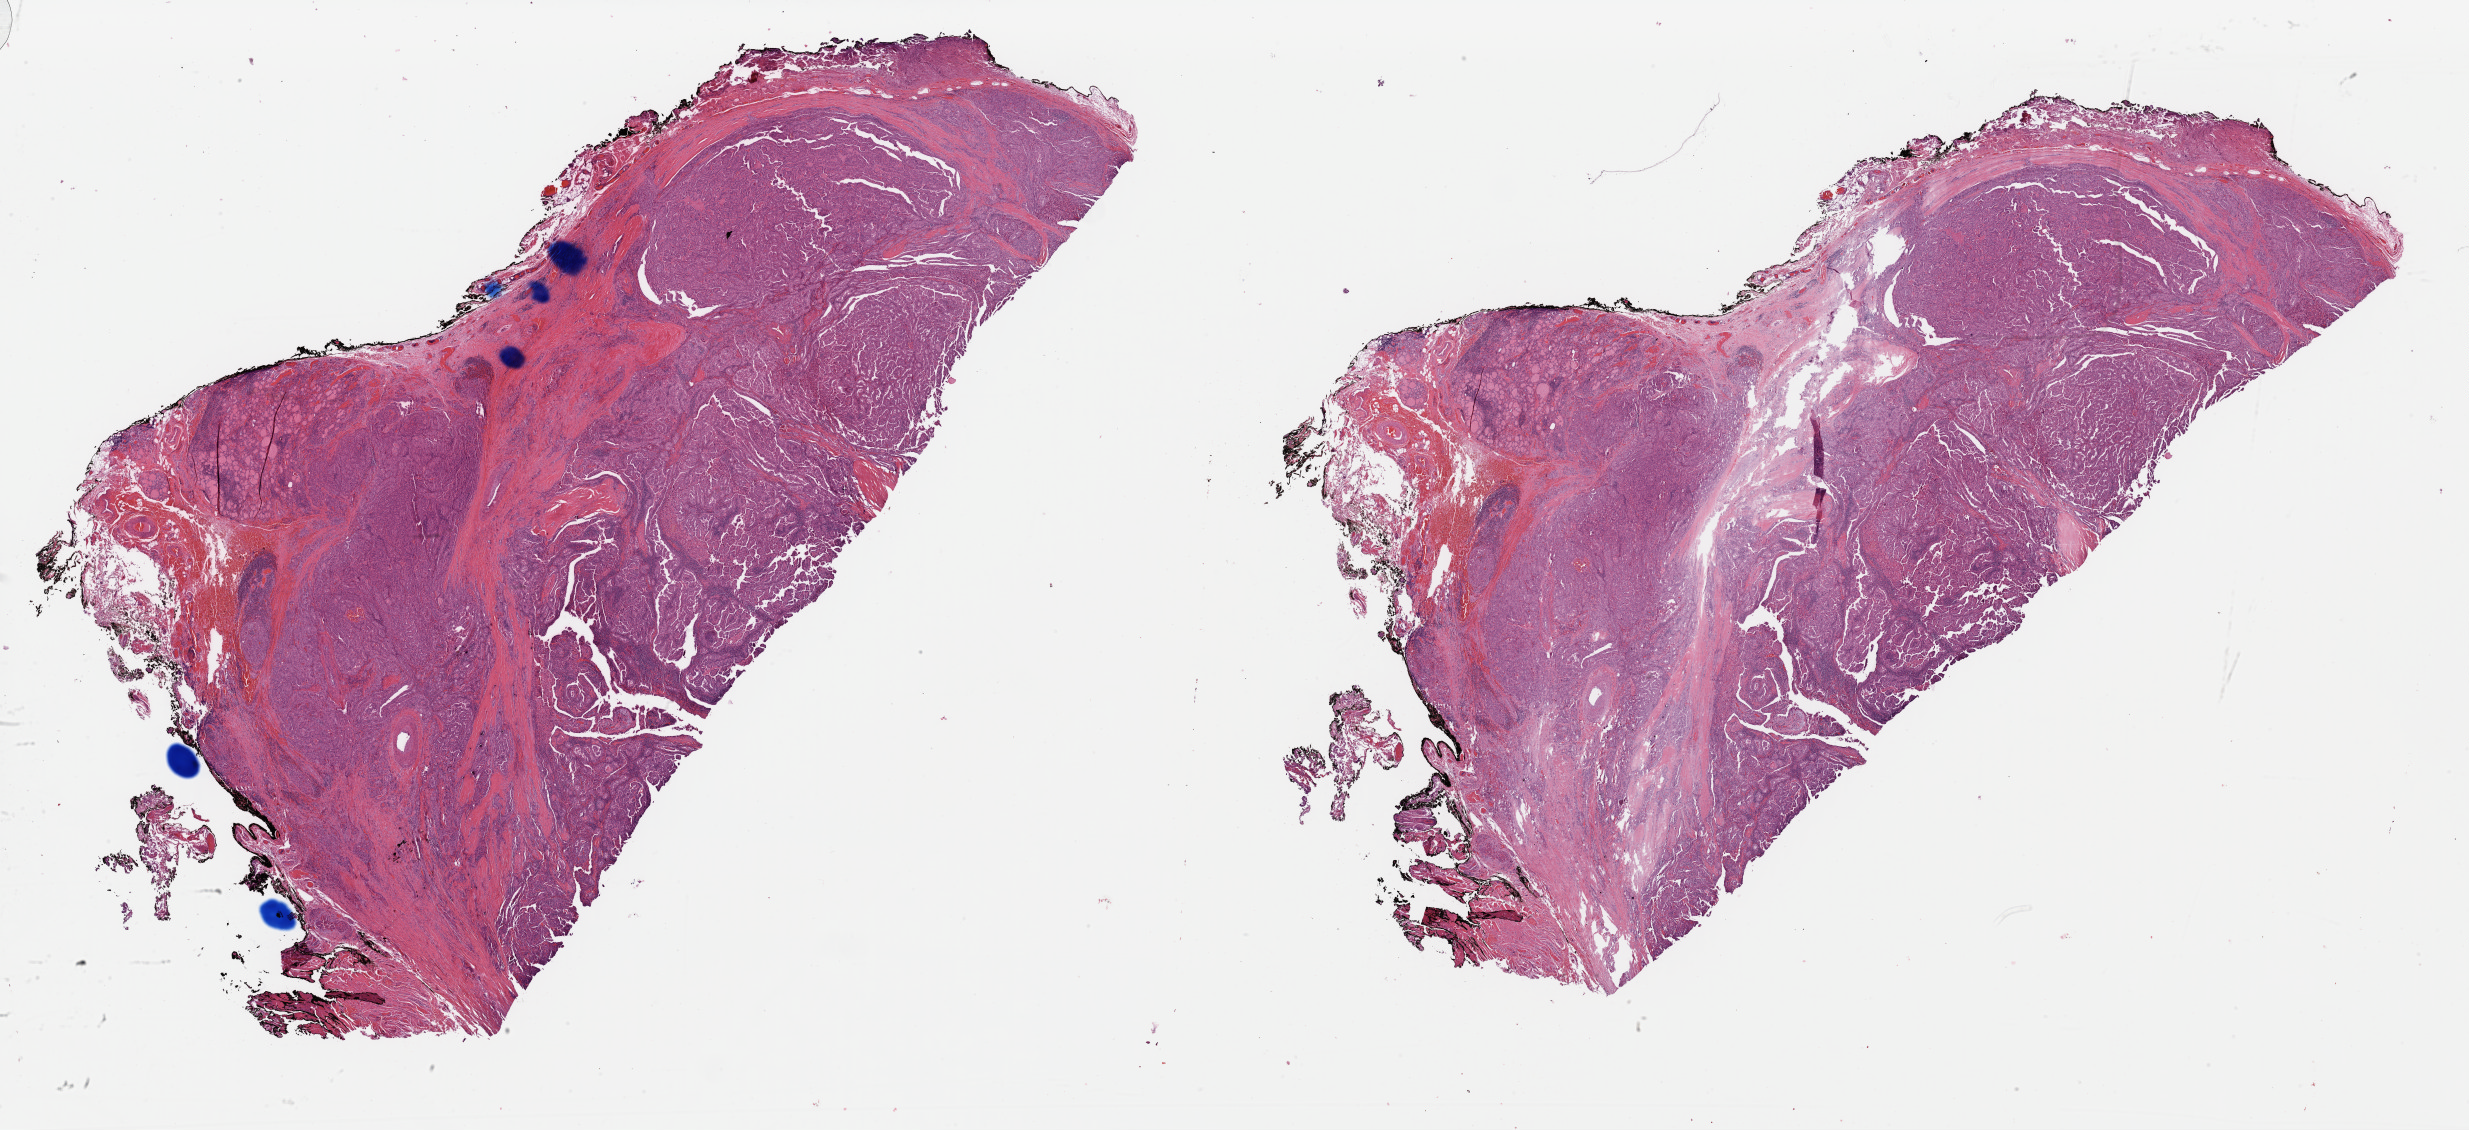
Digitized H&E-stained tissue section (whole slide) — low-resolution overview of the scanned area, about 39.0 x 17.9 mm (slide scanned at 40x); formalin-fixed paraffin-embedded (FFPE) diagnostic section; sample: primary tumour, thyroid. Patient: female, age at initial diagnosis 32 years.
AJCC pathologic stage: I (6th edition). Pathologic diagnosis: Papillary adenocarcinoma, NOS. Lymph nodes positive (case pathology): 3 of 12 examined. TNM: T3 N1a MX. Laterality: right.